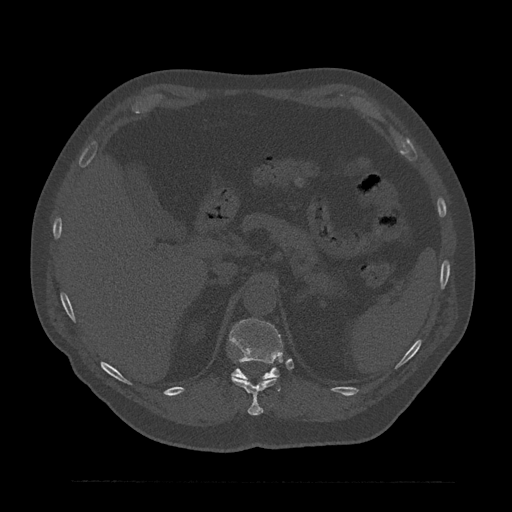
CT including the spine, one axial slice. Slice 262 of 797 in the series (ordered by position). Reconstruction kernel Br40s/3. Bone window (W 1800 / L 400 HU). 0.5 mm slice thickness. 512 × 512 image matrix, field of view 430 × 430 mm. Patient: male, 61 years. Case-level facts recorded for this patient, not image findings: primary cancer: prostate.
Outlined on this slice (semi-automatically segmented with operator editing):
- T11 vertebra: bounding box (x1, y1, x2, y2) in pixels: (231, 375, 278, 416)
- T12 vertebra: (230, 319, 283, 391)